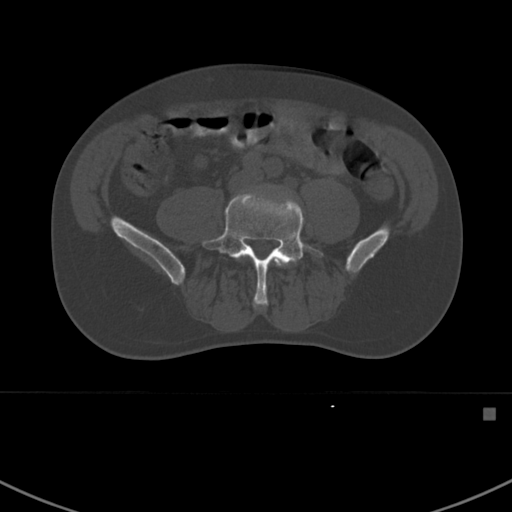
CT including the spine, one axial slice; position 225 of 412 along the scan axis; 120 kVp; bone window (W 1800 / L 400 HU); 1.5 mm slice thickness; 512 × 512 image matrix, field of view 358 × 358 mm. Patient: male, 59 years. From the clinical record (not read from this slice): primary cancer: prostate.
Annotated regions visible in this slice (semi-automatically segmented with operator editing):
- L4 vertebra: bounding box [x1, y1, x2, y2] px = [243, 255, 289, 267]
- L5 vertebra: [202, 191, 323, 307]